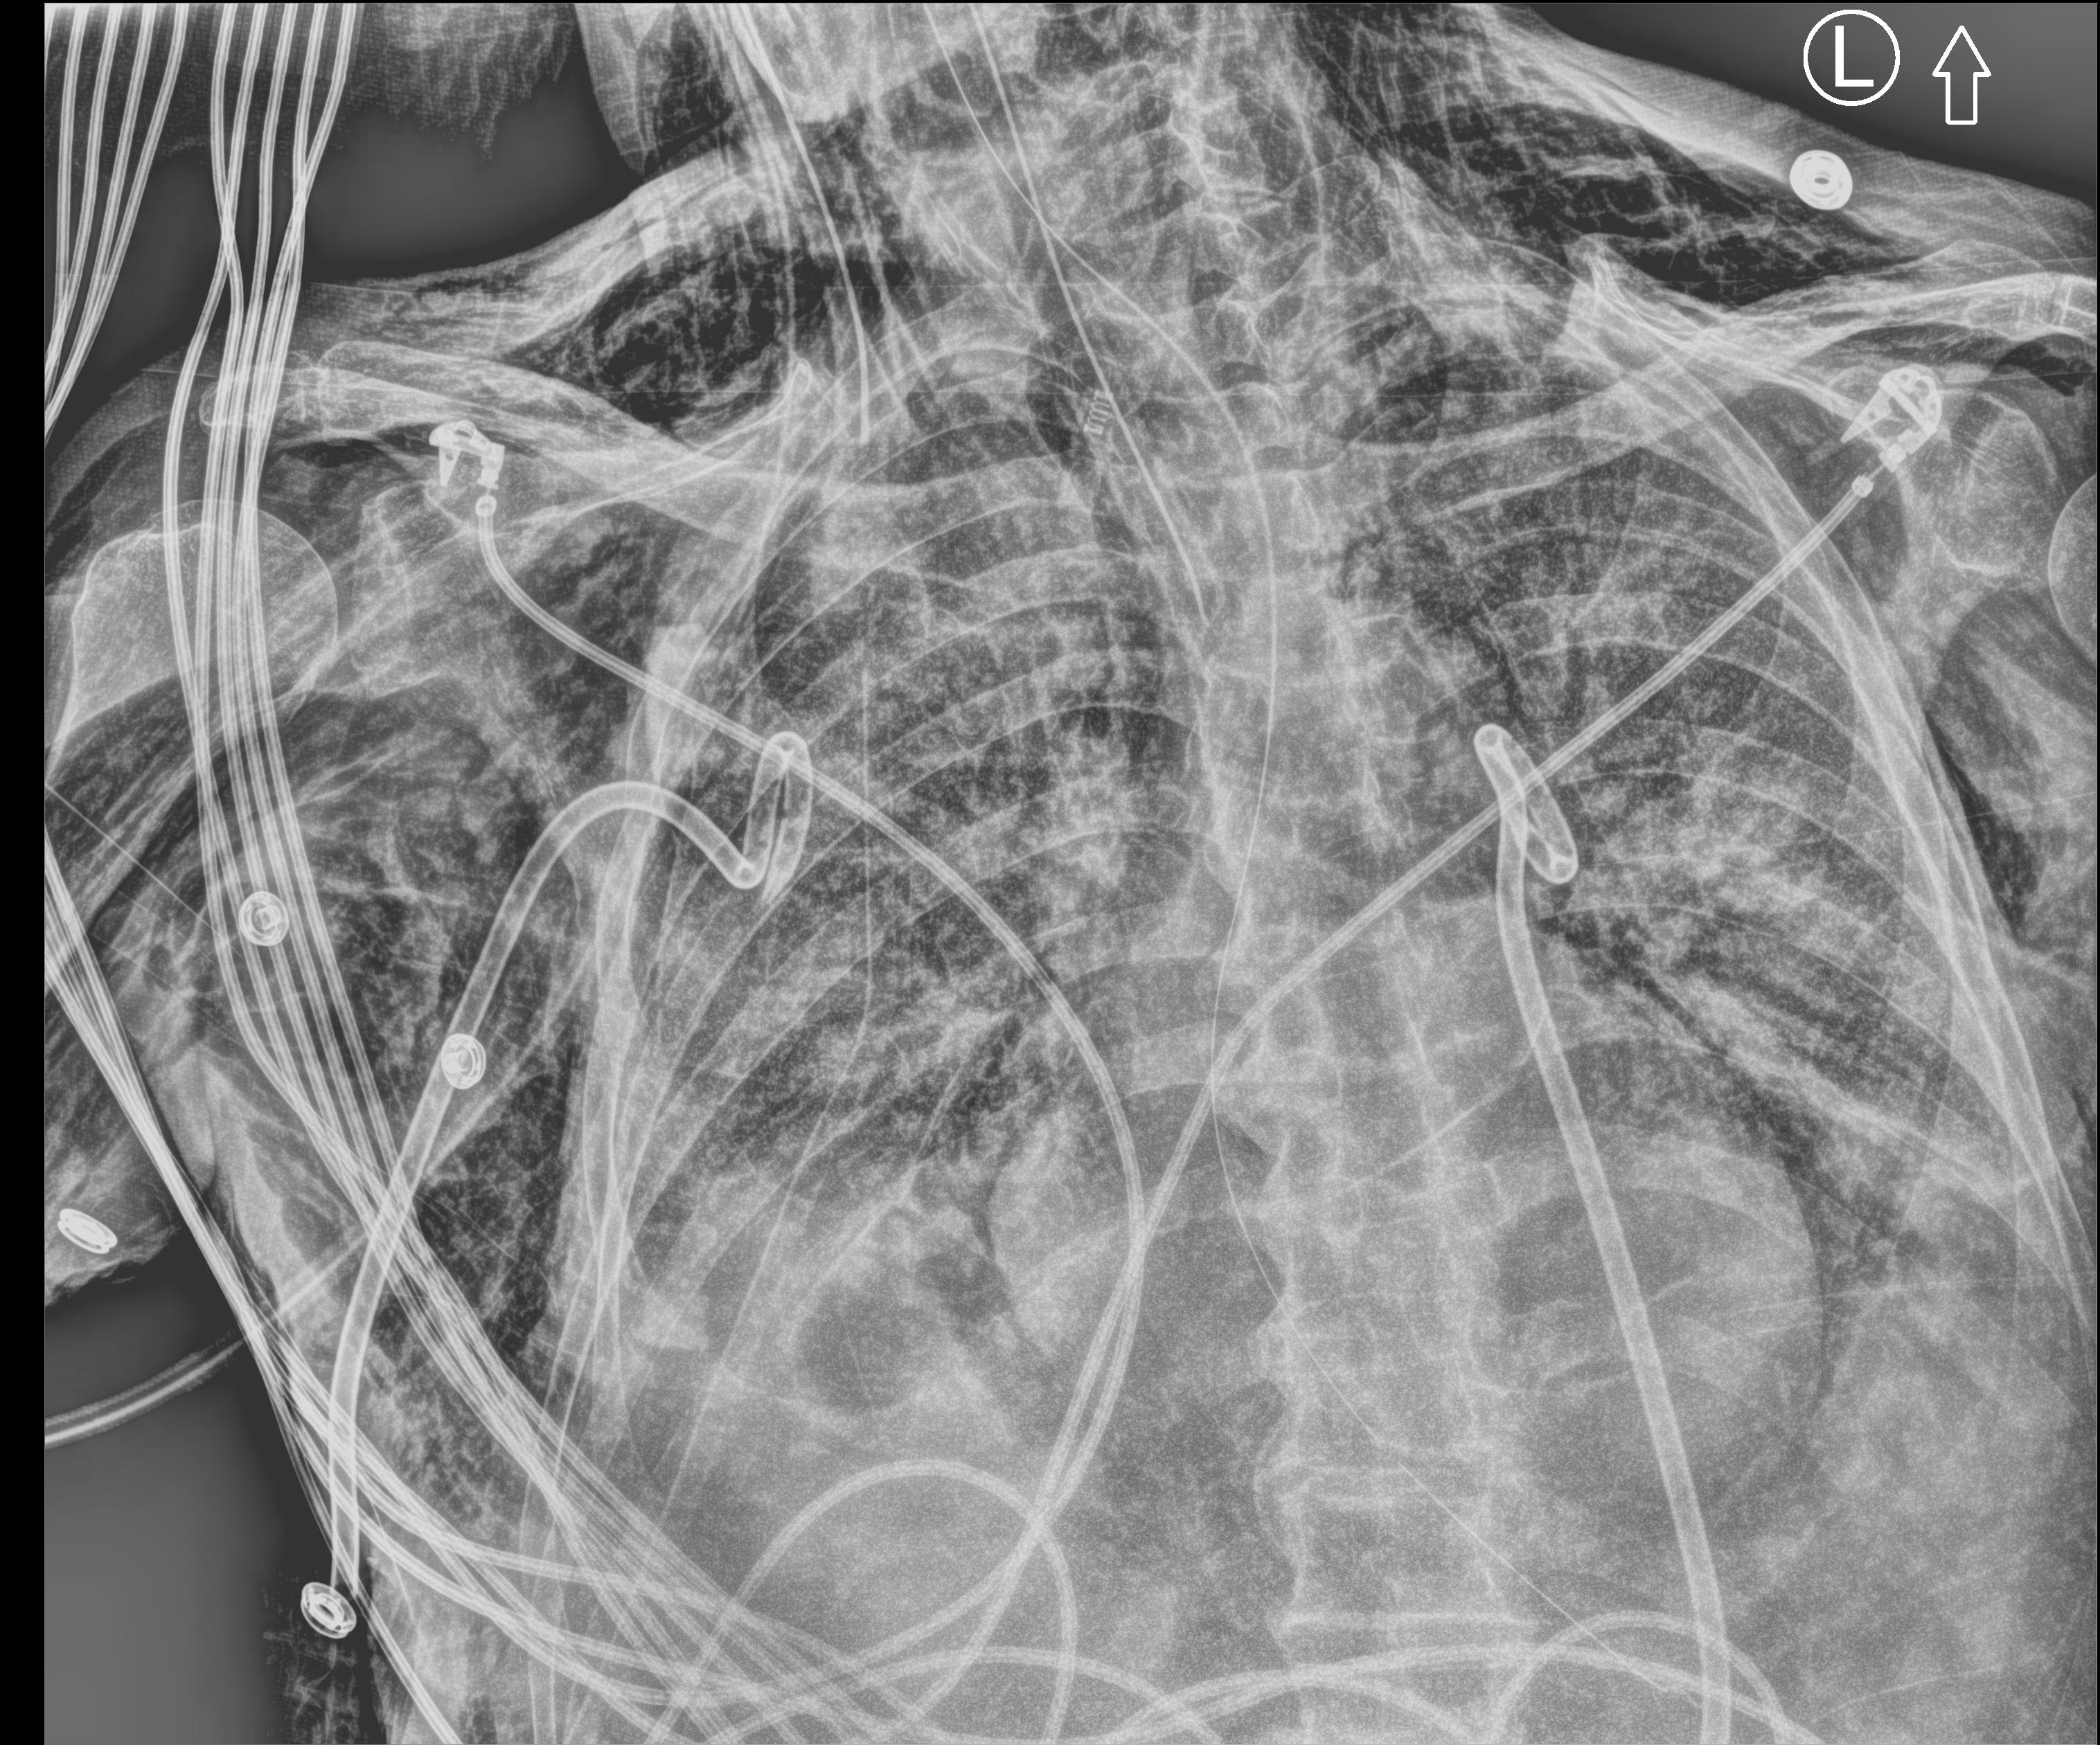
Portable chest radiograph, anteroposterior (AP) projection. Patient hospitalised with COVID-19; male, aged 75–90 years.
Admission-level facts for this patient (not findings on this image; timing relative to this image not recorded):
- mechanically ventilated during this hospital stay: yes
- smoking status (admission record): never